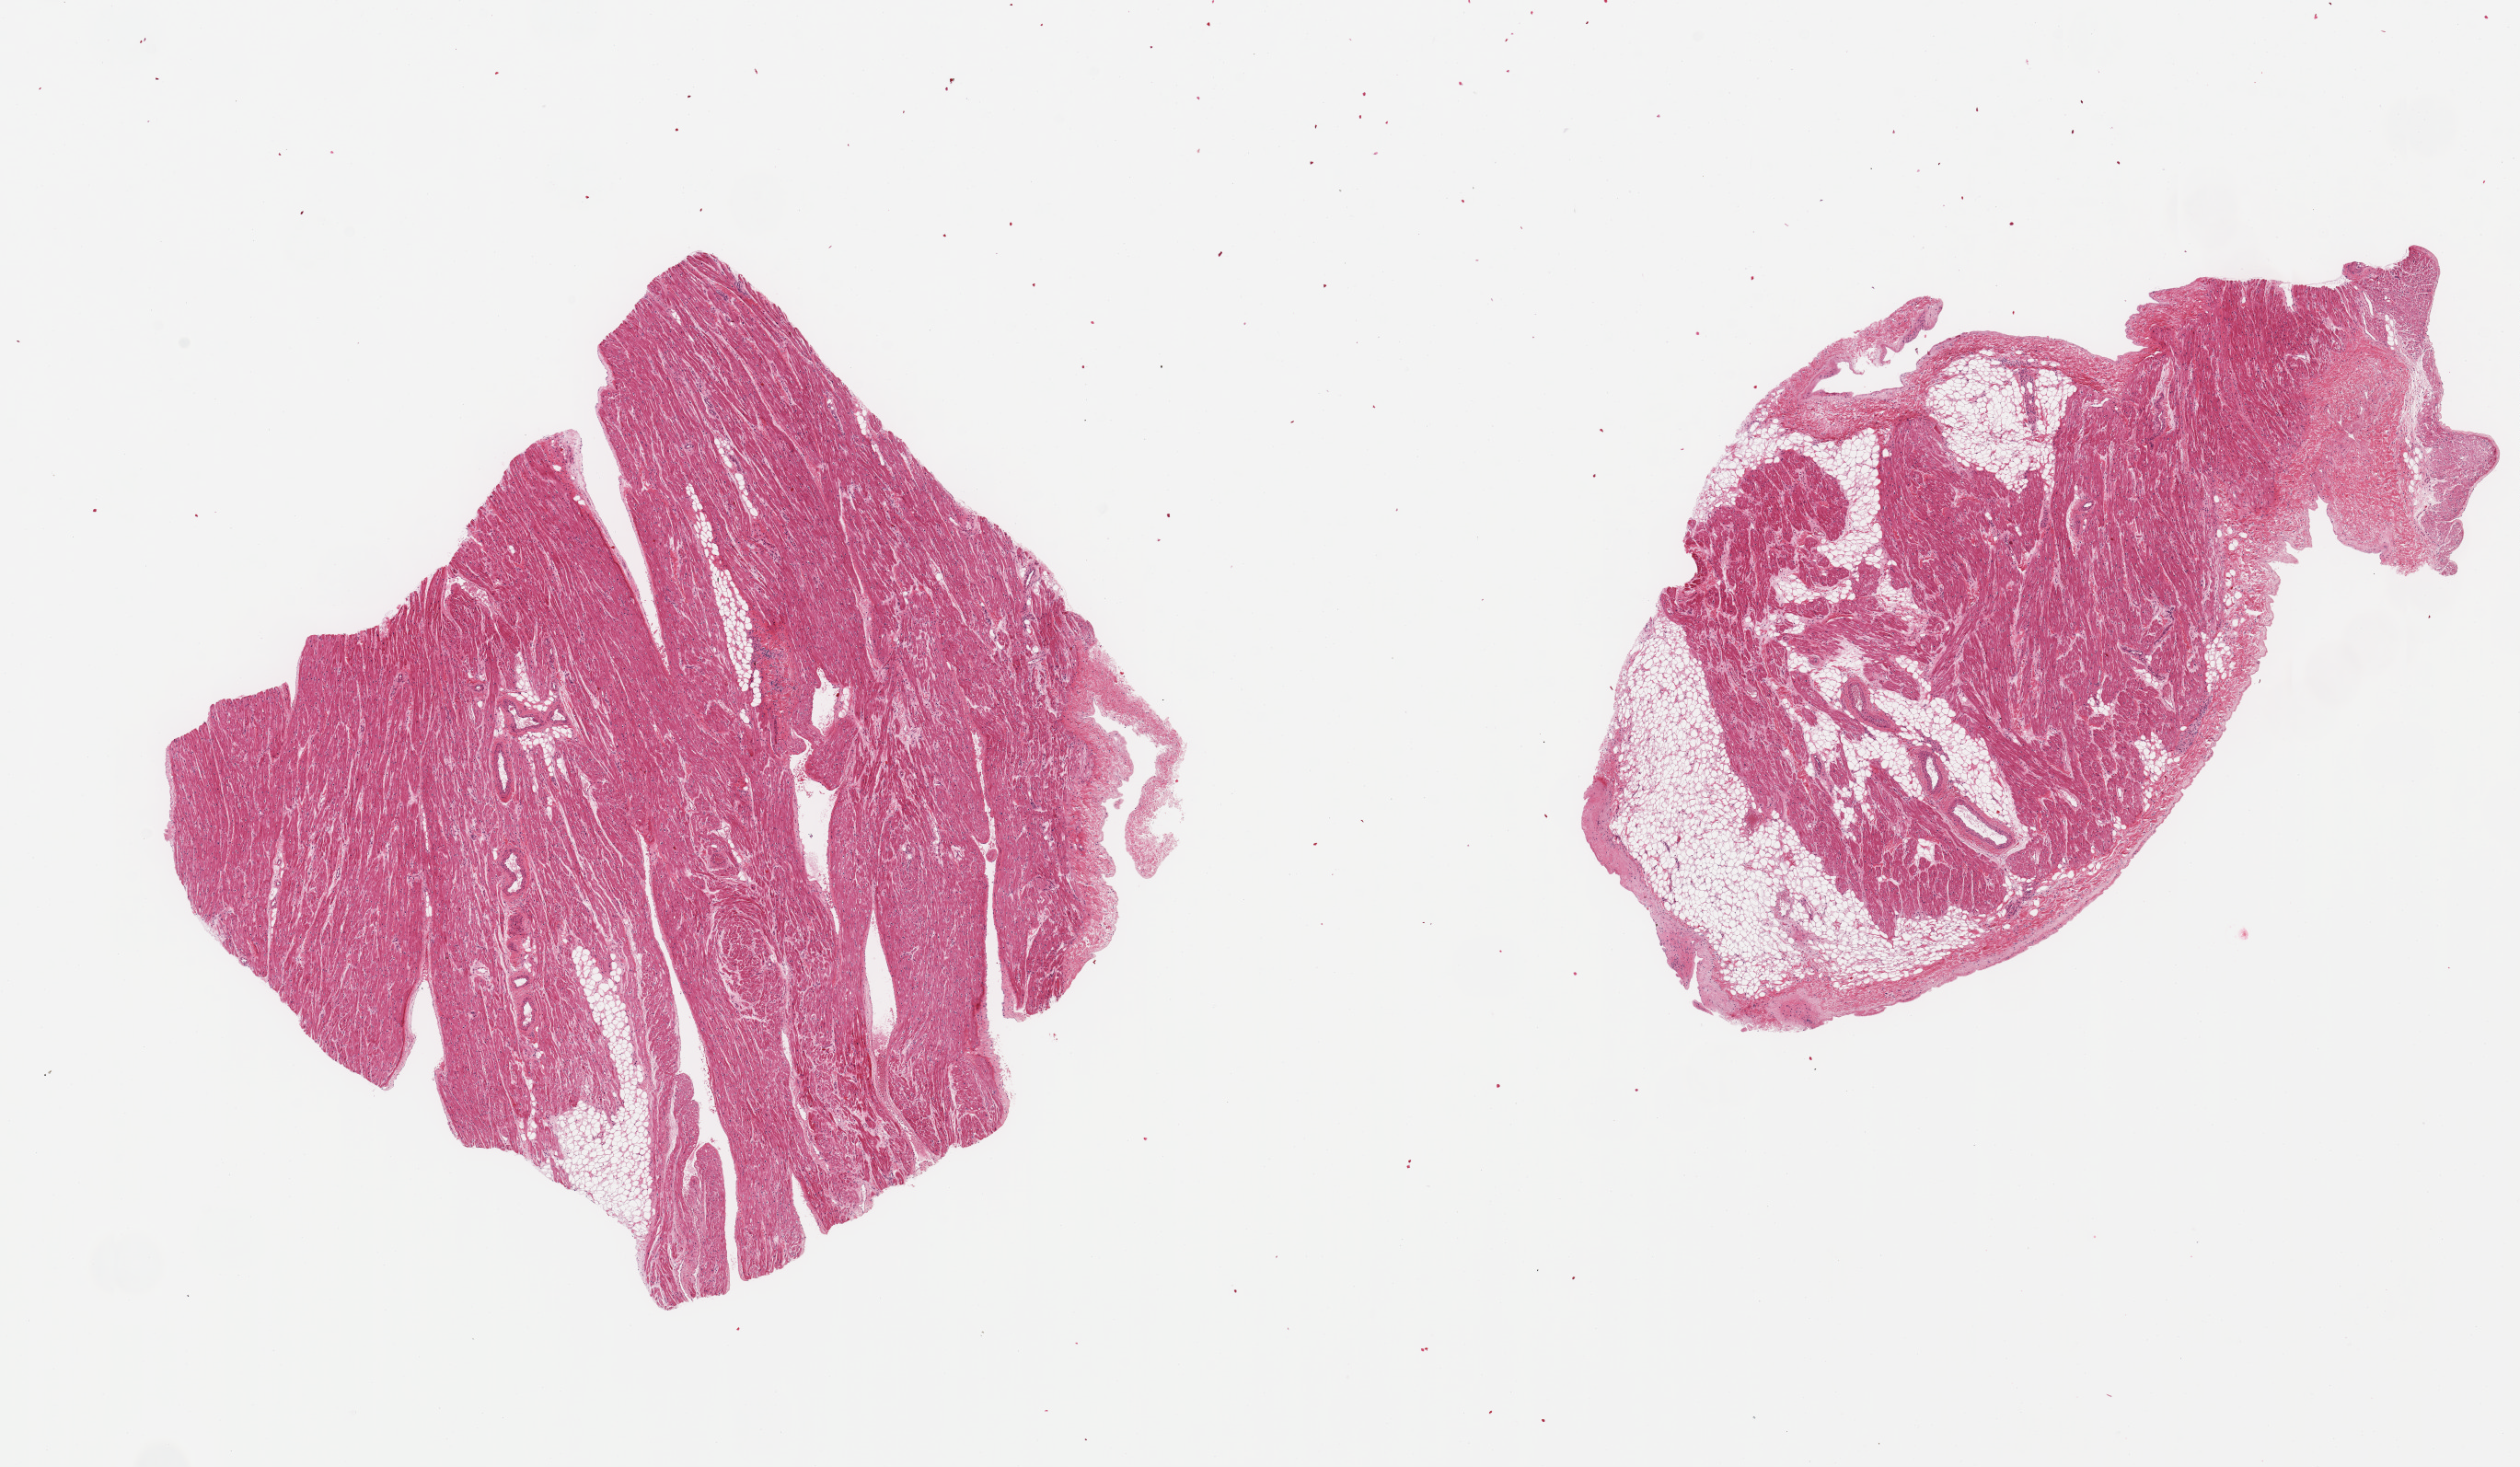
H&E whole-slide image, a low-resolution overview of the entire scanned area, about 21.7 x 12.6 mm (from a 20x scan). PAXgene-fixed, paraffin-embedded tissue. Section of auricular appendage (target tissue). Tissue donor sample. Male donor.
Review note (as recorded): 2 pieces; ~5% and 15% internal fat.